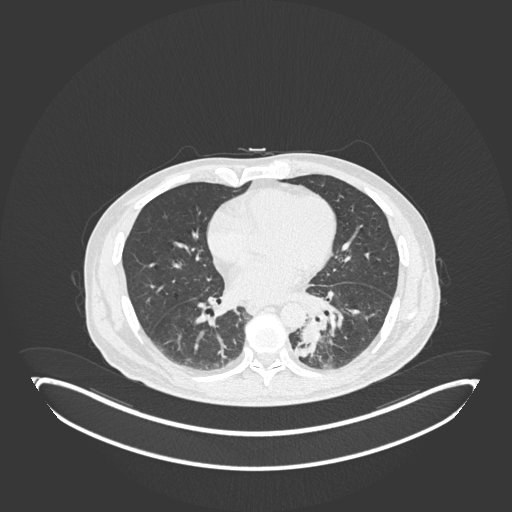
Chest CT, one axial slice; position 71 of 251 along the scan axis; reconstruction kernel B30f; lung window (W 1500 / L -600 HU); 1 mm slice thickness; 512 × 512 image matrix, field of view 500 × 500 mm. Male patient, age 72 years. From the clinical record (not read from this slice): clinical TNM (as recorded): T2b N0 M1.
Outlined on this slice (rectangle marked by the reading radiologist):
- lung tumour (recorded histology: adenocarcinoma): bounding box [x1, y1, x2, y2] px = [297, 318, 323, 360]